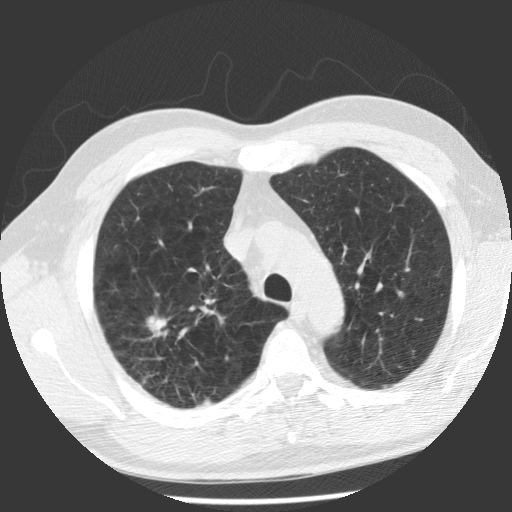
Low-dose screening chest CT, one axial slice; position 85 of 112 along the scan axis; 140 kVp; lung window (W 1500 / L -600 HU); 2.5 mm slice thickness; 512 × 512 image matrix.
Annotated regions visible in this slice (outlined manually by an expert reader):
- lesion 1 (tumor, upper lobe of right lung): bounding box (x1, y1, x2, y2) in pixels: (146, 316, 165, 335)